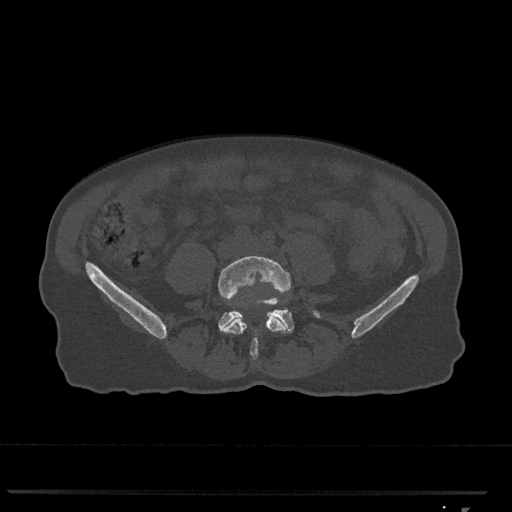
CT including the spine, one axial slice. Position 182 of 793 along the scan axis. Bone window (W 1800 / L 400 HU). 0.5 mm slice thickness. 512 × 512 image matrix. Patient: female, 62 years. From the clinical record (not read from this slice): primary cancer: renal.
Outlined on this slice (semi-automatically segmented with operator editing):
- L4 vertebra: bounding box (x1, y1, x2, y2) in pixels: (218, 255, 291, 360)
- L5 vertebra: (218, 298, 320, 333)